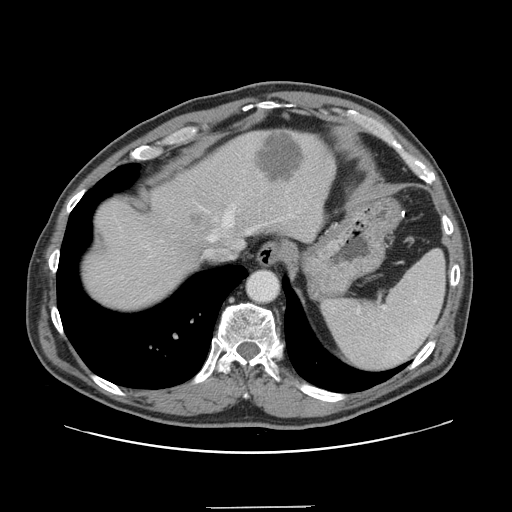
Contrast-enhanced abdominal CT, one axial slice. 120 kVp. Soft-tissue window (W 400 / L 40 HU). 2.5 mm slice thickness. 512 × 512 image matrix. Male patient, age 64 years. From the clinical record (not read from this slice): diagnosis: colorectal cancer liver metastases, imaged before liver resection; multiple liver metastases: yes; largest metastasis: 3.5 cm; disease in both lobes: yes.
Outlined on this slice (outlined manually by an expert reader):
- hepatic veins: bounding box [x1, y1, x2, y2] px = [223, 214, 230, 226]
- liver: [83, 129, 333, 312]
- planned liver remnant (the part of the liver to remain after resection): [82, 136, 260, 312]
- liver metastasis: [192, 215, 205, 225]
- liver metastasis: [257, 133, 304, 183]